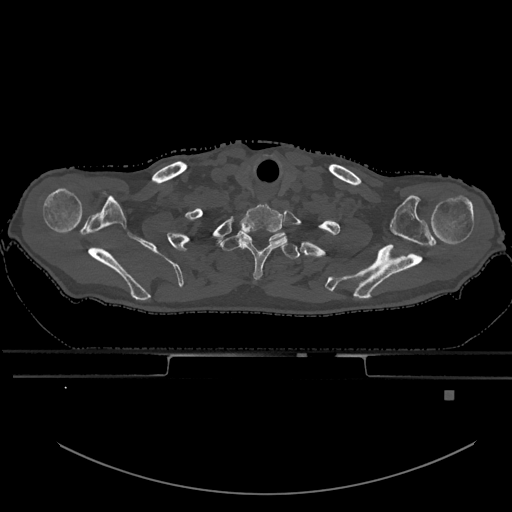
CT including the spine, one axial slice; position 557 of 969 along the scan axis; bone window (W 1800 / L 400 HU); 512 × 512 image matrix, field of view 456 × 456 mm. Patient: male, 82 years. Case-level facts recorded for this patient, not image findings: primary cancer: prostate.
Structures marked on this image (semi-automatically segmented with operator editing):
- T1 vertebra: bounding box <221,233,300,259> (left, top, right, bottom; pixels)